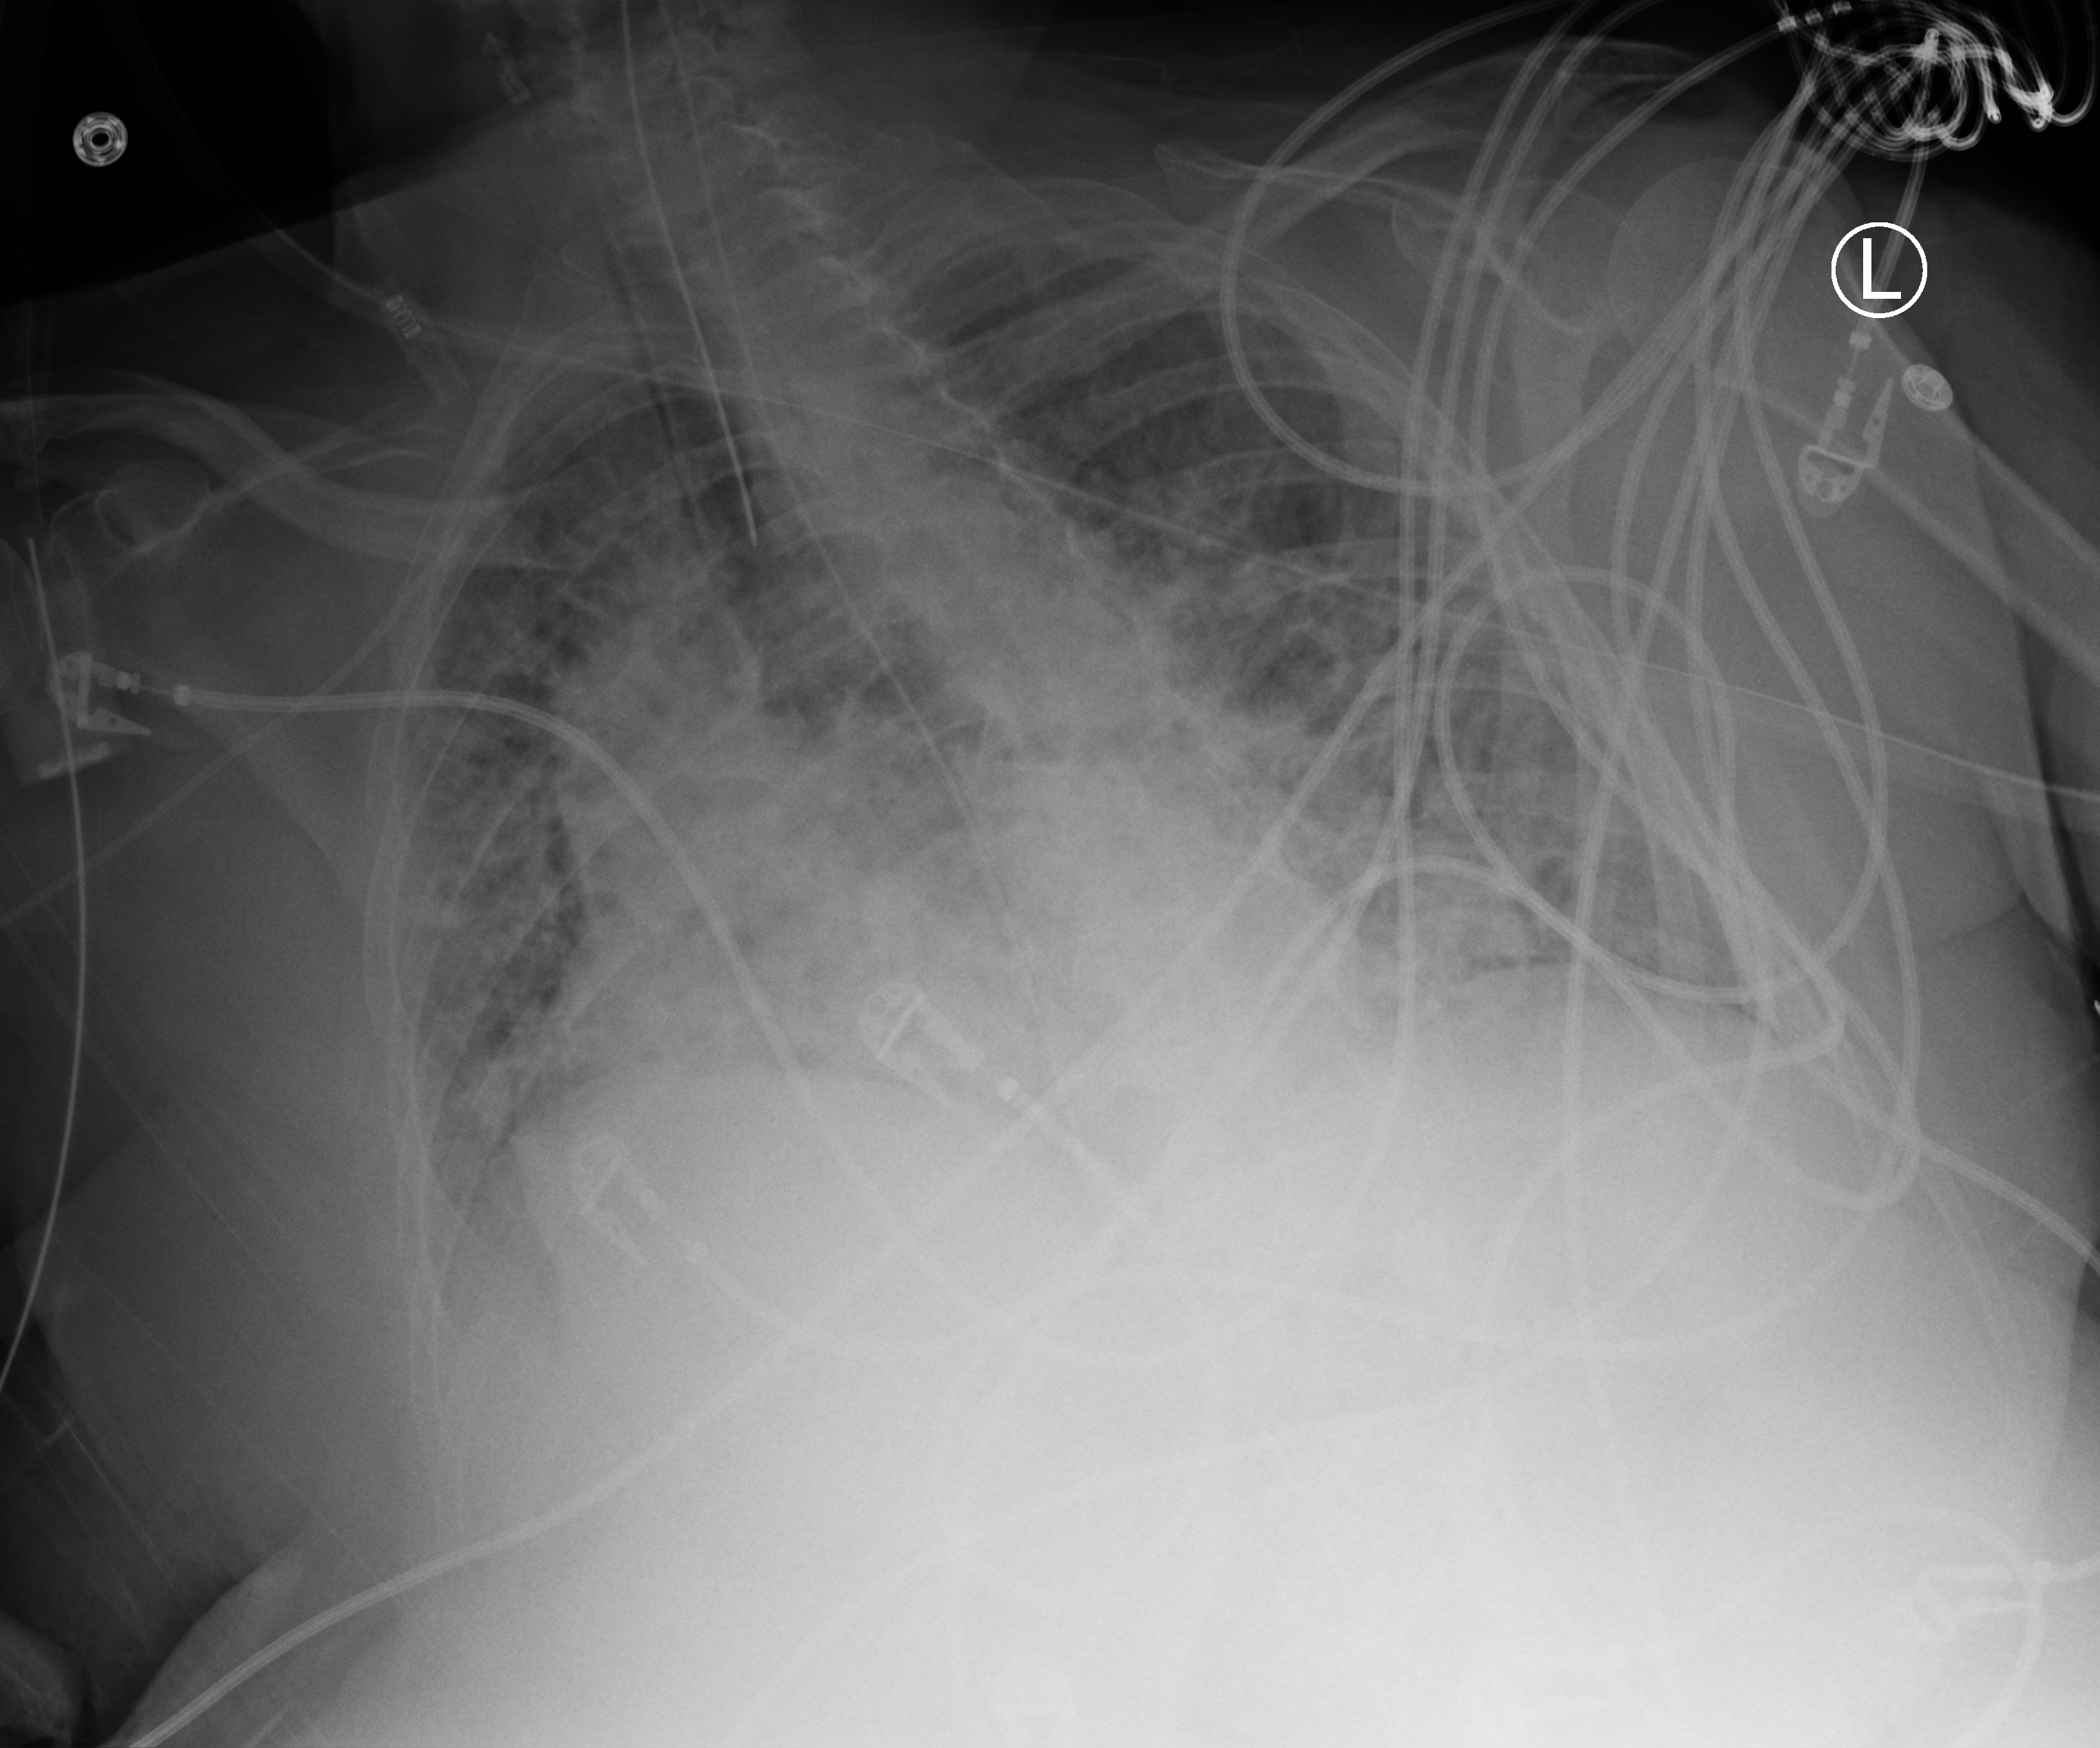
Portable chest radiograph, anteroposterior (AP) projection. Patient hospitalised with COVID-19; female, aged 75–90 years.
From the hospital-stay record, not from the radiograph (when in the stay this image was taken is not recorded):
- mechanically ventilated during this hospital stay: yes
- admitted to intensive care during this hospital stay: yes